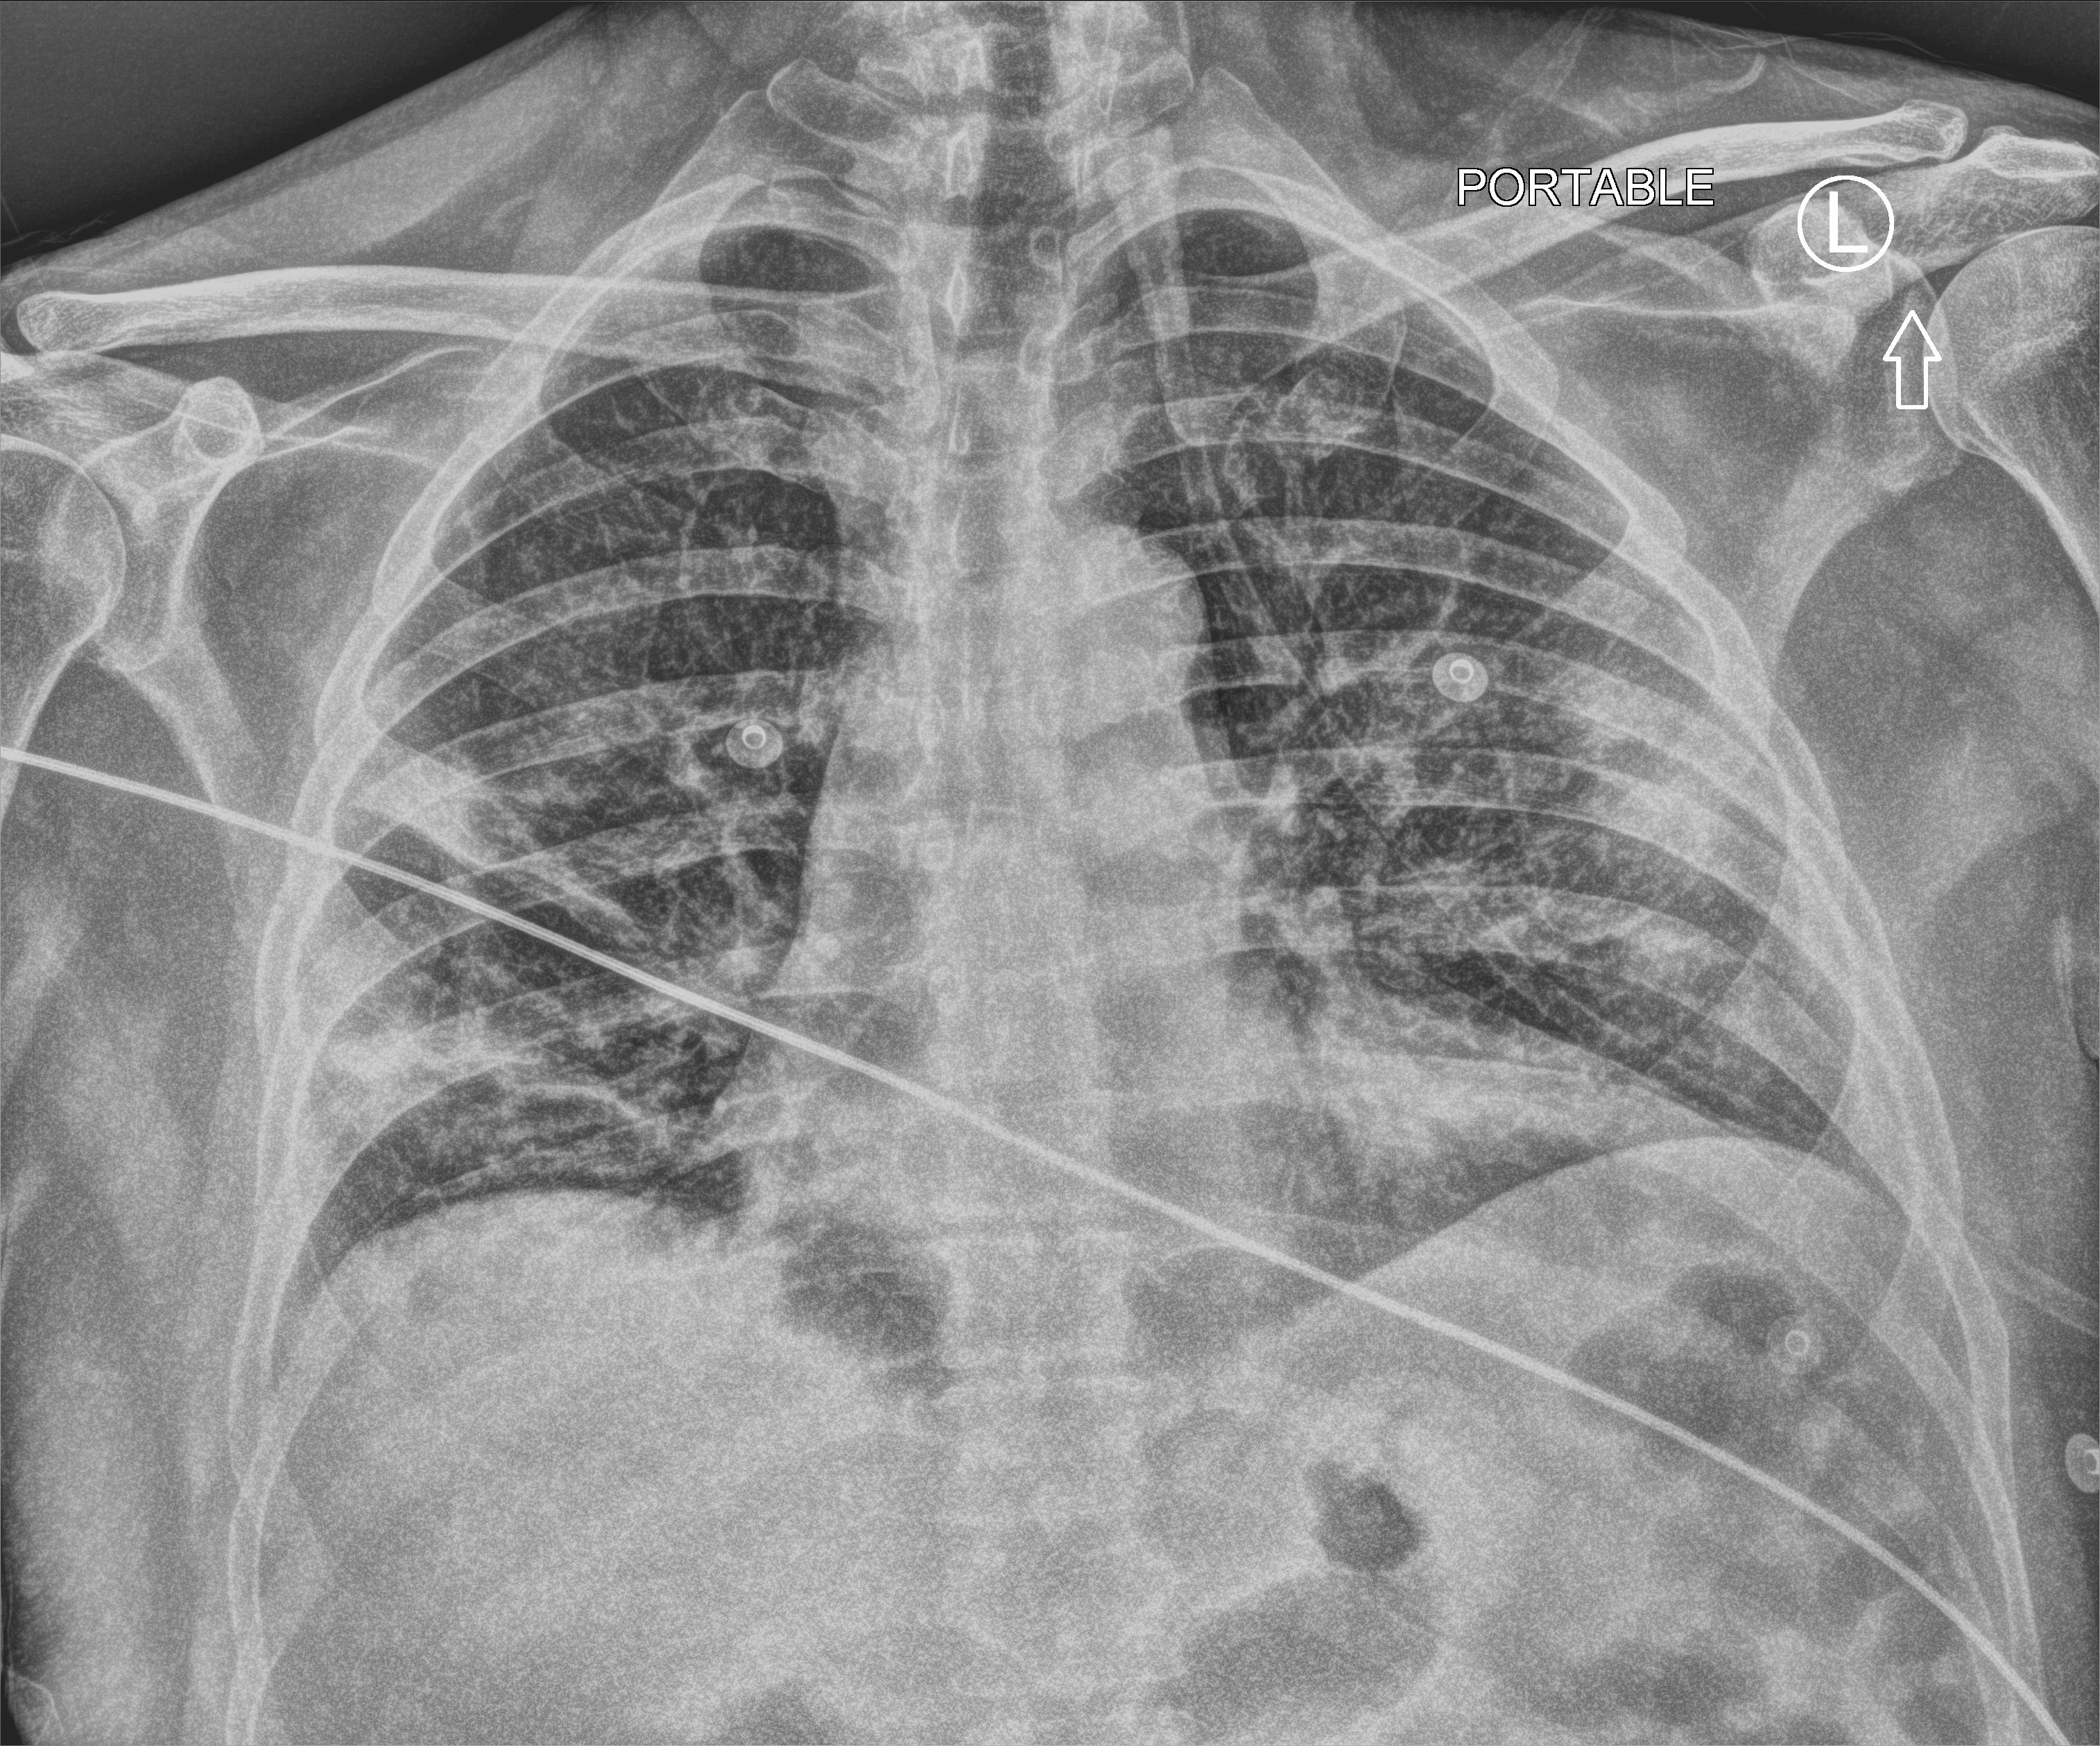
Portable chest radiograph, anteroposterior (AP) projection. Patient hospitalised with COVID-19; male, aged 60–74 years.
From the hospital-stay record, not from the radiograph (when in the stay this image was taken is not recorded): length of hospital stay: 11 days; admitted to intensive care during this hospital stay: no.